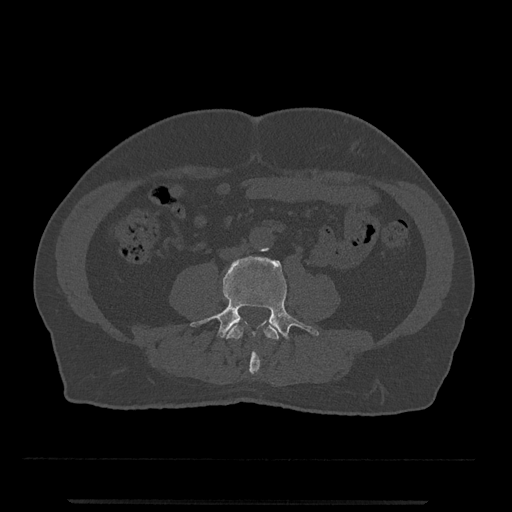
CT including the spine, one axial slice; position 156 of 797 along the scan axis; reconstruction kernel Br40s/3; bone window (W 1800 / L 400 HU); 0.5 mm slice thickness; 512 × 512 image matrix, field of view 419 × 419 mm. Patient: male, 63 years. From the clinical record (not read from this slice): primary cancer: prostate.
Structures marked on this image (semi-automatically segmented with operator editing):
- L3 vertebra: bounding box <227,324,281,375> (left, top, right, bottom; pixels)
- L4 vertebra: <190,256,319,340>